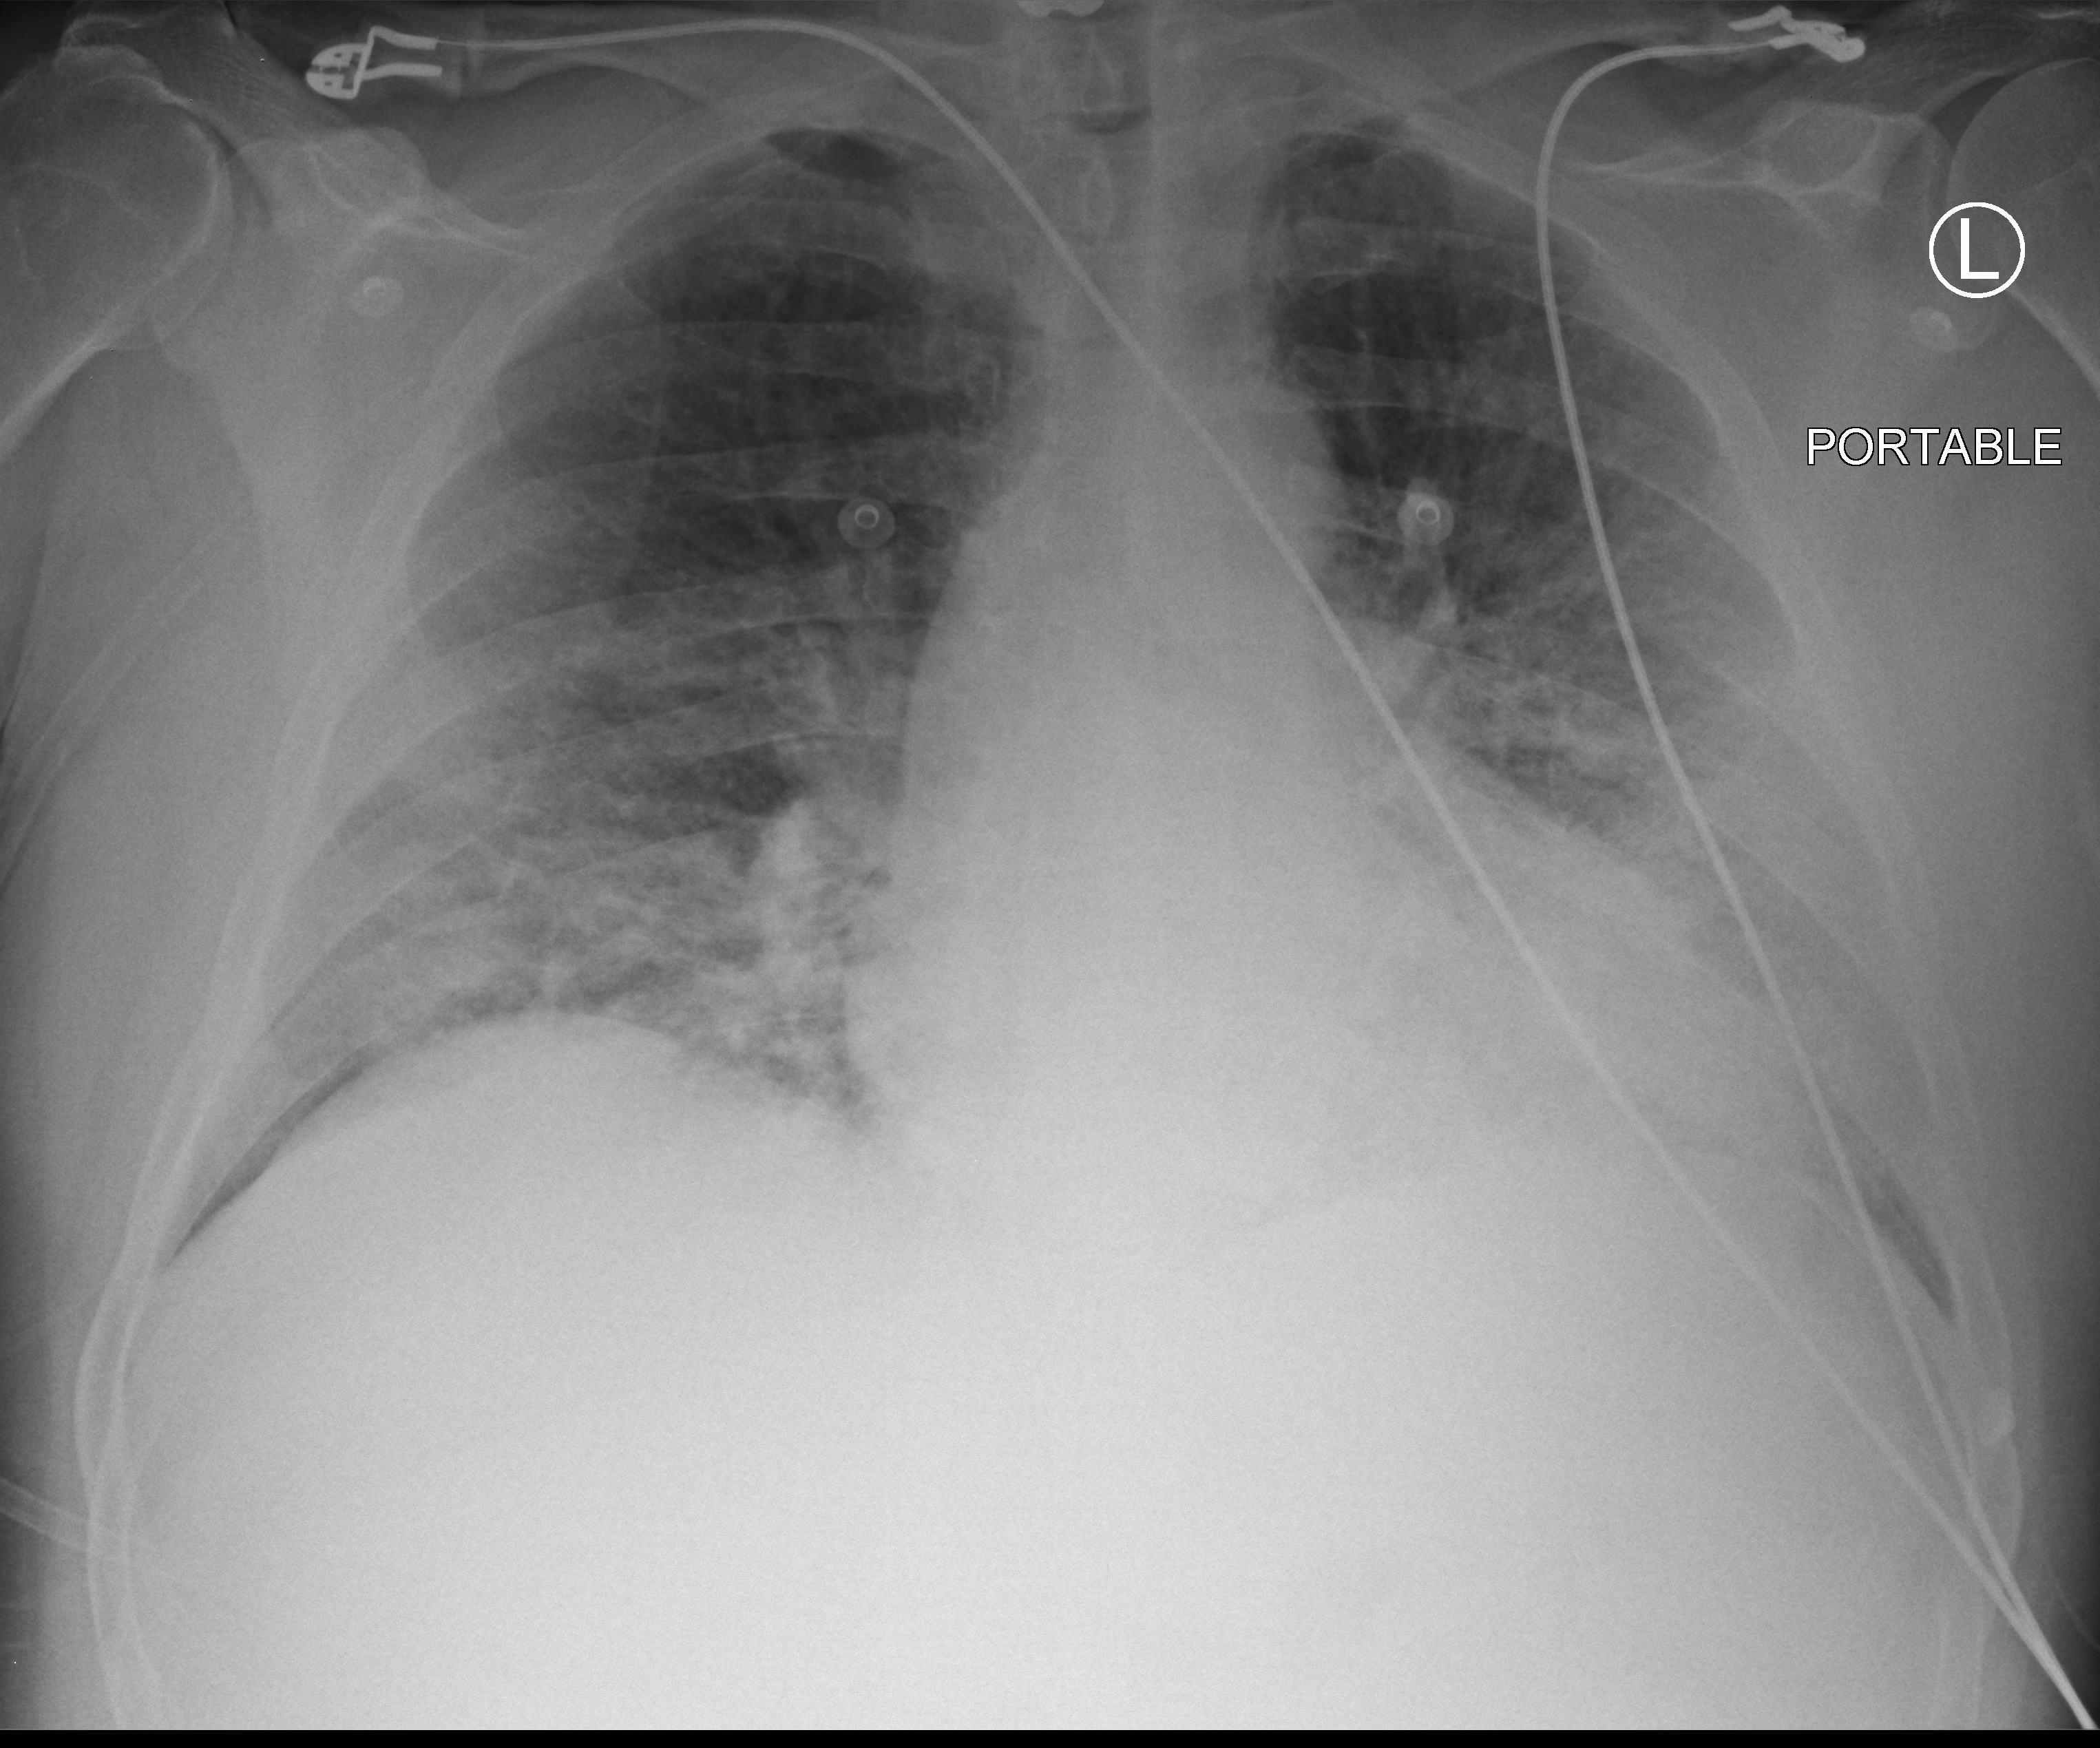
Bedside chest radiograph (computed radiography), anteroposterior (AP) projection. Male patient hospitalised with COVID-19, age 60–74 years.
Admission-level facts for this patient (not findings on this image; timing relative to this image not recorded): smoking status (admission record): current; mechanically ventilated during this hospital stay: no; diabetes (admission record): no.